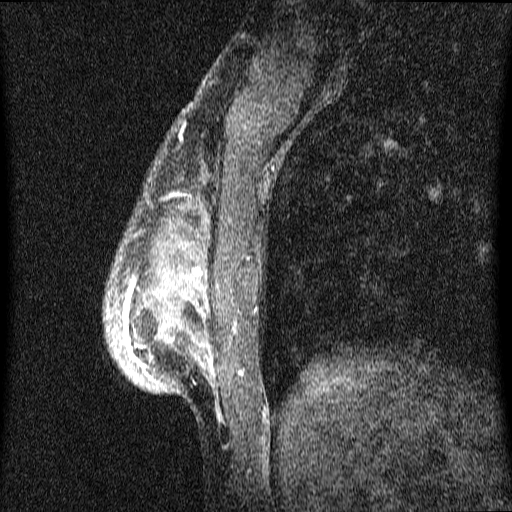
Breast MRI (dynamic contrast-enhanced), one sagittal slice. Position 16 of 64 along the scan axis. Dynamic contrast-enhanced series, image 2 of 4 at this slice position (ordered by acquisition). 1.5 T. TE 4.2 ms, TR 9.1 ms. 2 mm slice thickness. 512 × 512 image matrix, field of view 180 × 180 mm. Female patient, age 33 years.
Annotated regions visible in this slice (semi-automatically segmented with operator editing):
- analysis volume of interest (the breast-tissue region the enhancement analysis was run in; not a lesion): box from (x=104, y=151) to (x=259, y=424) px
- tumour enhancement mask (voxels above the 70 % enhancement threshold inside the analysis volume of interest): (x=124, y=269)–(x=215, y=382)